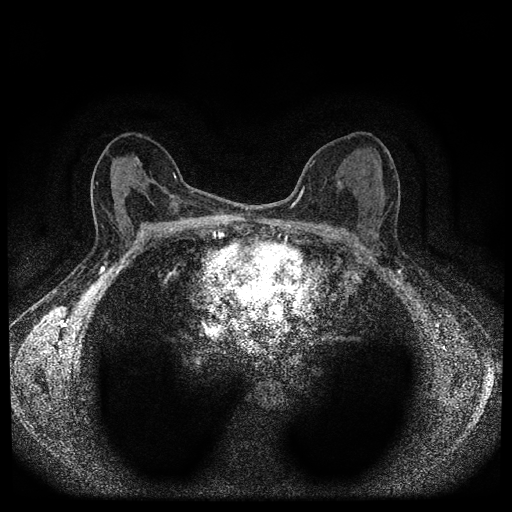
Breast MRI (dynamic contrast-enhanced, multi-phase), one axial slice. Slice 53 of 112 in the series (ordered by position). Dynamic contrast-enhanced series, time point 2 of 5 at this slice position (early post-contrast). 1.5 T. TE 2.7 ms, TR 5.4 ms. 512 × 512 image matrix. Female patient, age 61 years.
Annotated regions visible in this slice (semi-automatic segmentation, software-assisted and operator-edited):
- breast lesion (labelled benign in the annotation): bounding box (x1, y1, x2, y2) in pixels: (337, 181, 343, 188)